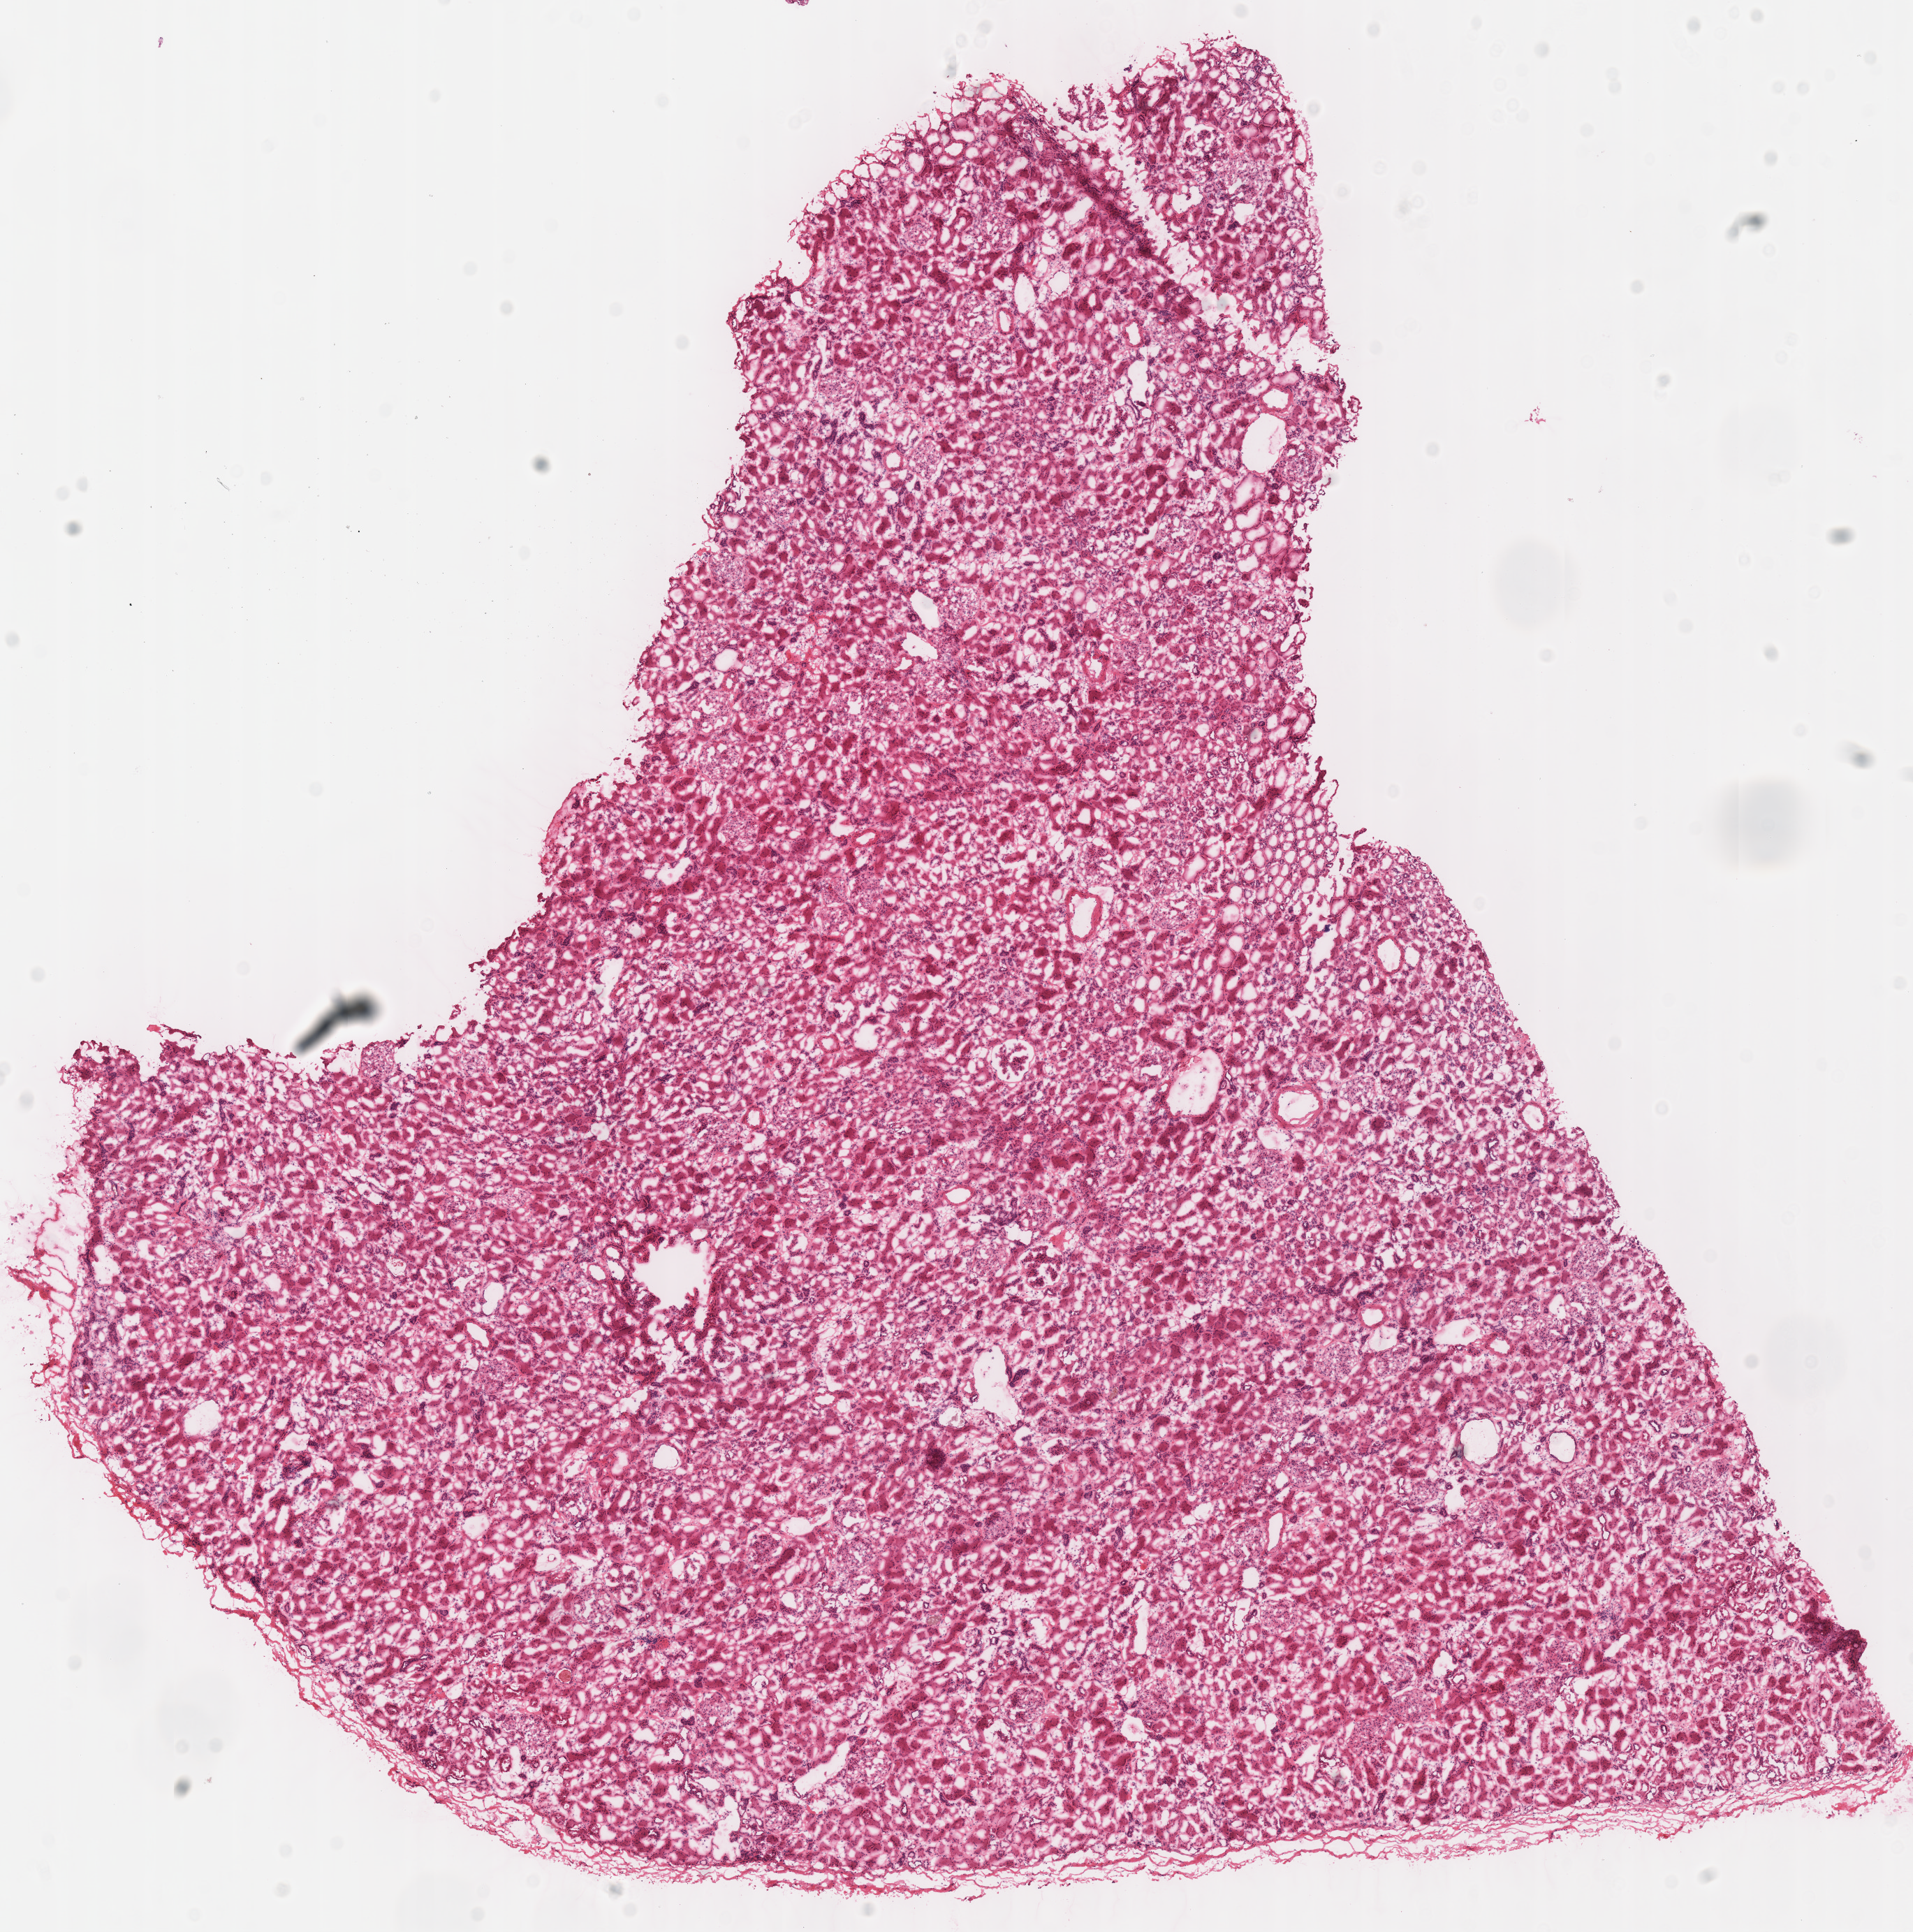
H&E-stained whole-slide image, whole scanned area (about 10.8 x 10.9 mm, slide scanned at 40x) shown as a low-resolution overview; frozen section; solid tissue normal (non-tumour tissue) sample from the kidney. Female patient; age at initial diagnosis 56 years. Inflammatory infiltration, as recorded: lymphocyte infiltration 2%, monocyte infiltration 5%, neutrophil infiltration 0%.
This section: solid tissue normal sample (biorepository sample class). Patient diagnosis: Renal cell carcinoma, chromophobe type.